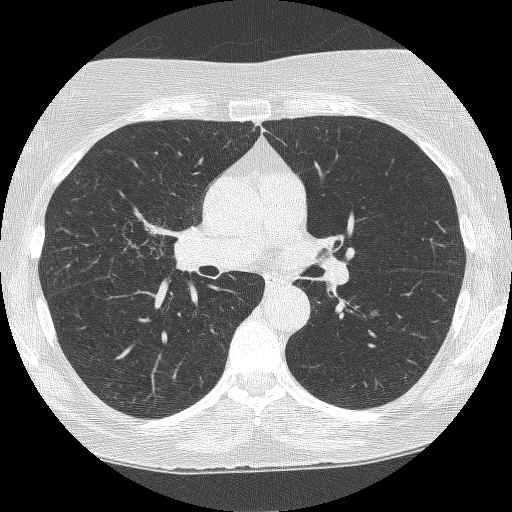
Chest CT (low-dose screening protocol), one axial image; second annual screen; lung window (W 1500 / L -600 HU); 1.25 mm slice thickness; lung (sharp) reconstruction kernel (BONE); 120 kVp; 512 × 512 image matrix, field of view 308 × 308 mm. Female participant, aged 64 years at enrolment.
Lesion marked by an expert reader, bounding box <117,206,201,286> (left, top, right, bottom; pixels). The screening reader recorded 4 non-calcified nodules or masses ≥4 mm on this exam (right upper lobe, right upper lobe, right upper lobe, left upper lobe); which of them this box marks is not recorded. Official screen result: positive, other. Participant outcome: lung cancer diagnosed 381 days after this screen (after the third annual screen) — adenocarcinoma, NOS, right upper lobe, right middle lobe, right hilum, stage IV (AJCC 6th edition), 85 mm at pathology.